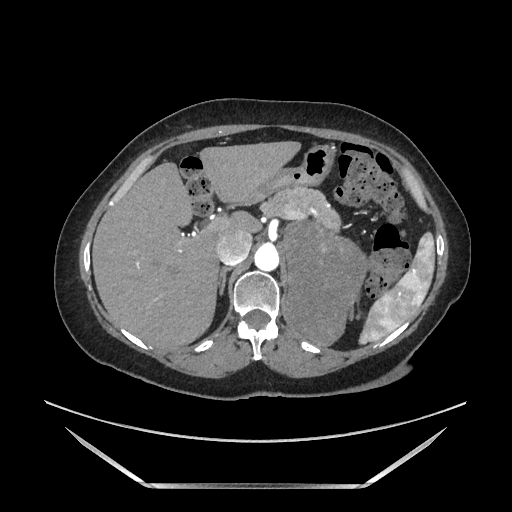
Contrast-enhanced abdominal CT, one axial slice. Position 121 of 205 along the scan axis. Soft-tissue window (W 400 / L 40 HU). 512 × 512 image matrix, field of view 440 × 440 mm. Female patient. From the clinical record (not read from this slice): diagnosis: adrenocortical carcinoma; tumour side: left adrenal; tumour size at pathology: 12.5 cm; Ki-67 index: 39 %; stage (as recorded): 3.
Structures marked on this image (semi-automatically segmented with operator editing):
- mass: bounding box <288,221,365,343> (left, top, right, bottom; pixels)